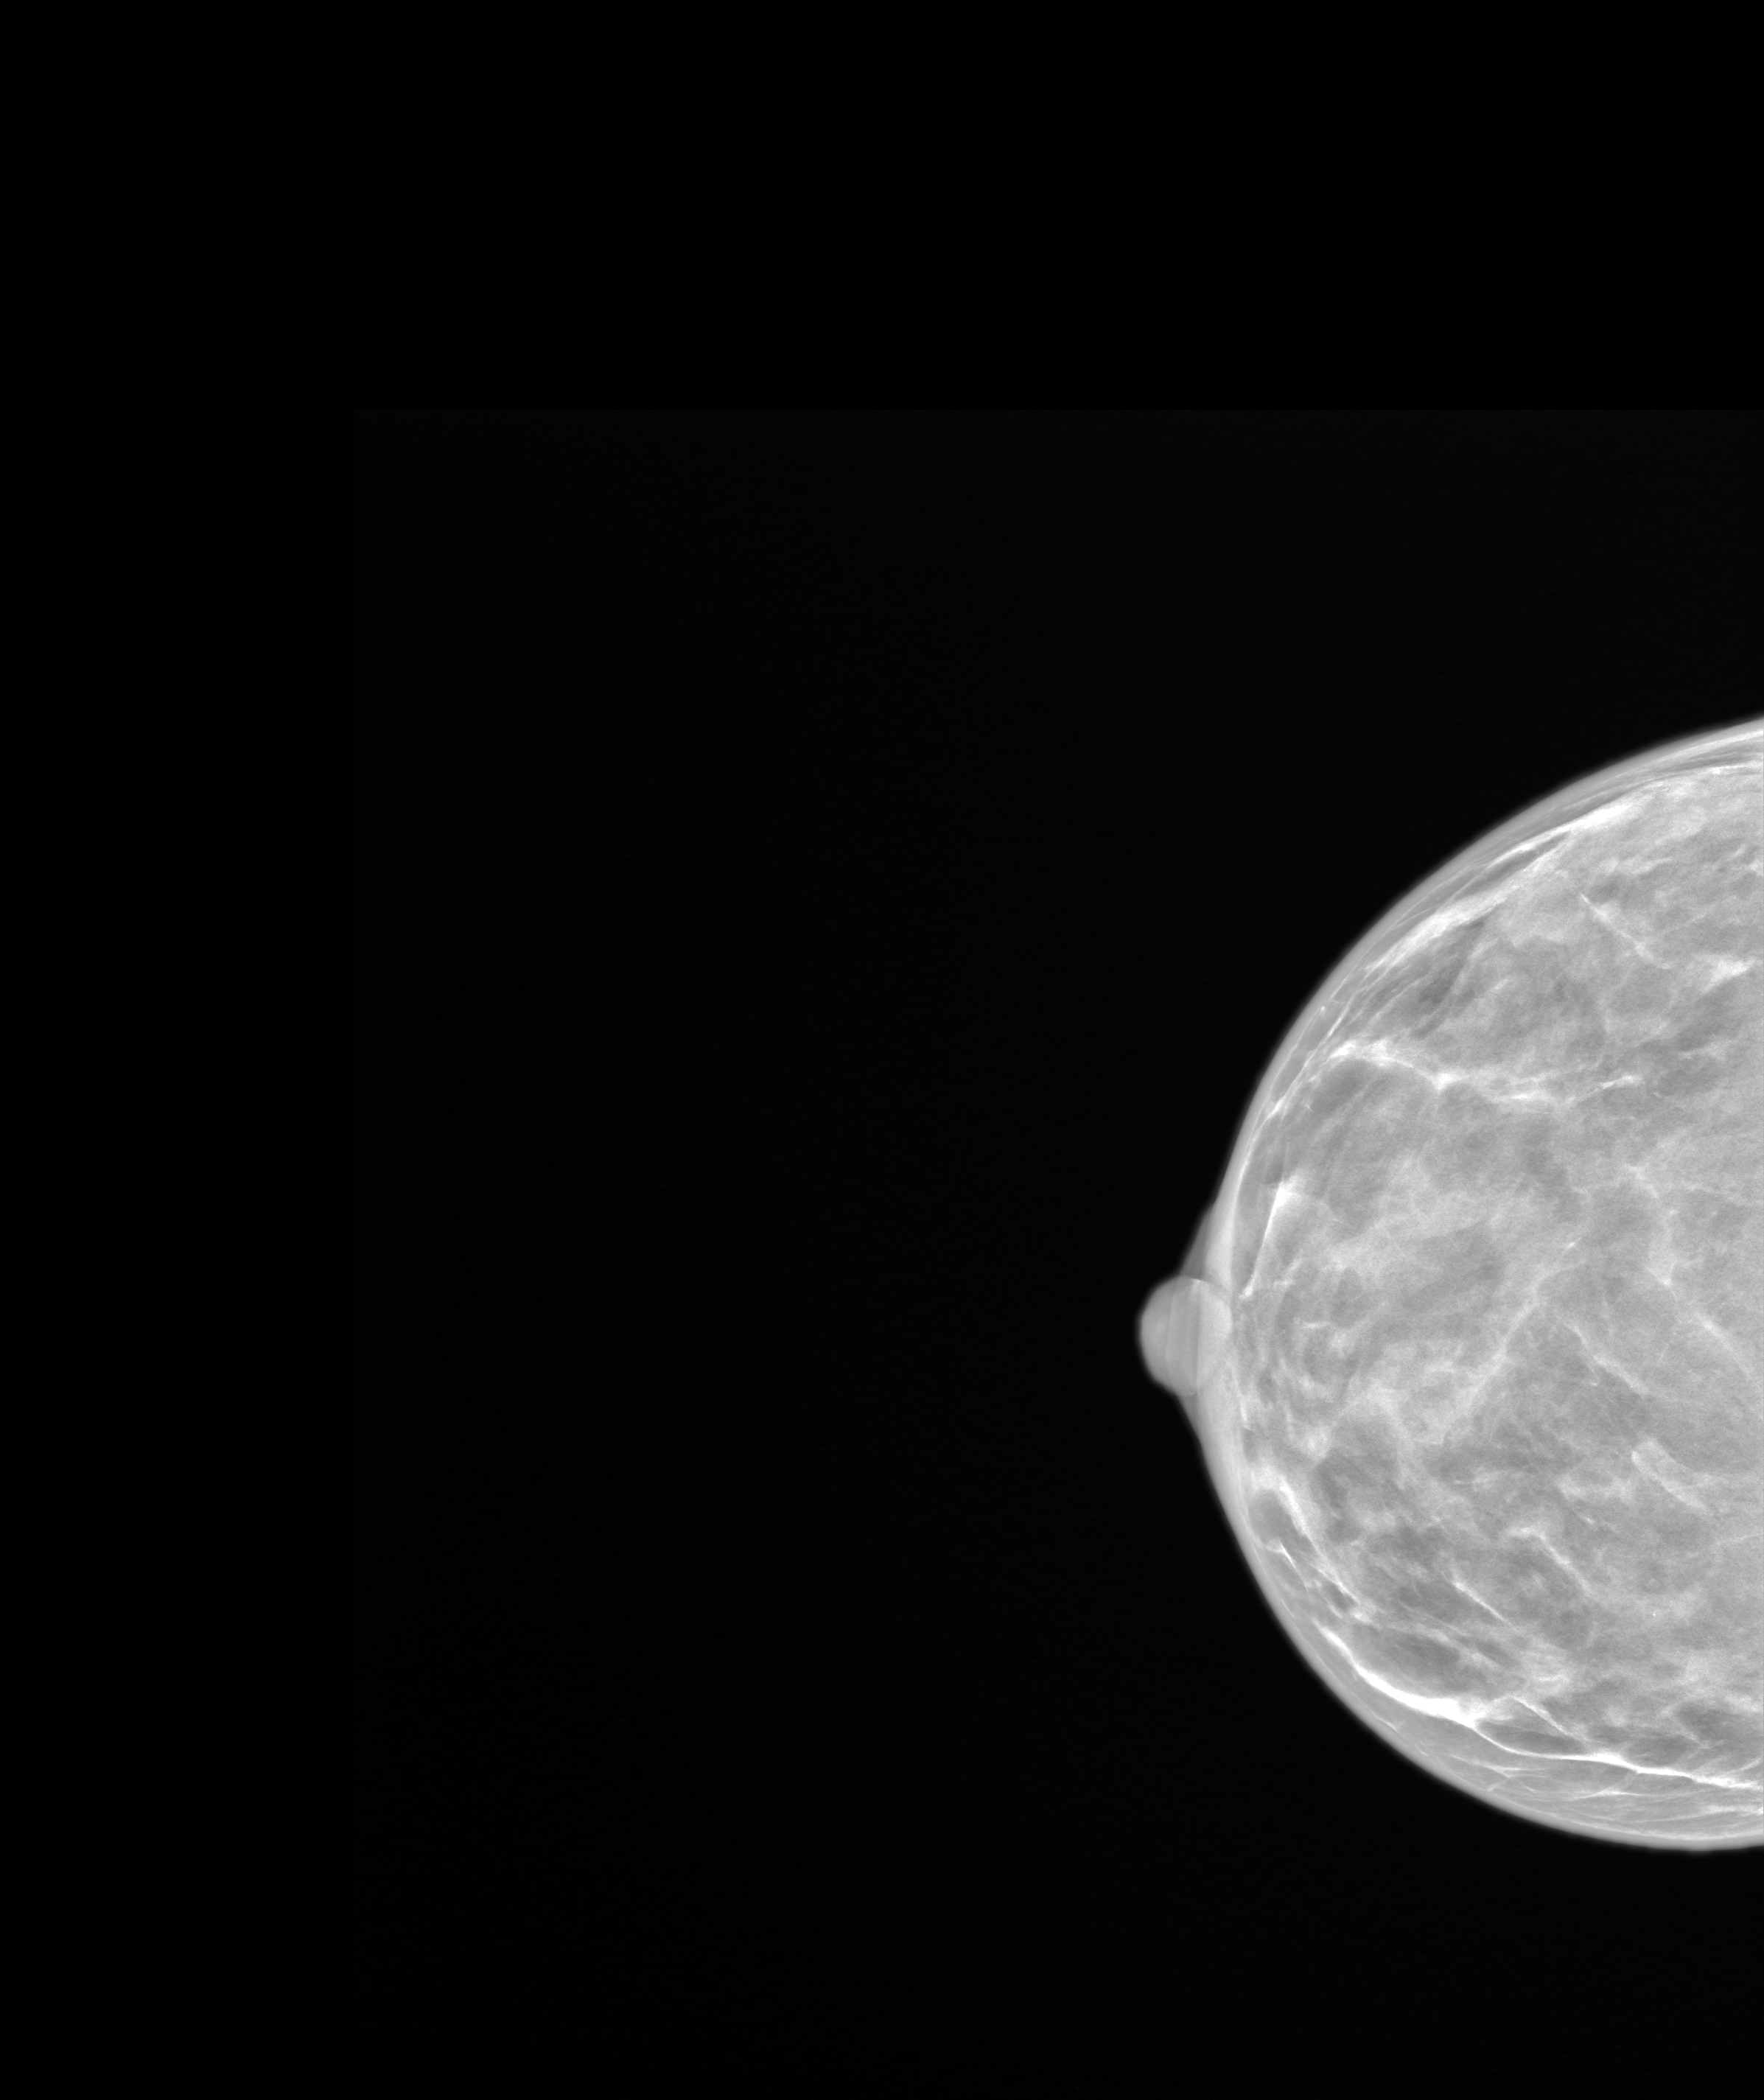
Annual screening mammography examination; system: SenoIris_1SP2(440). Patient: female, 46 years.
Image type: synthesized 2-D view from tomosynthesis. Breast: right. Projection: cranio-caudal projection.